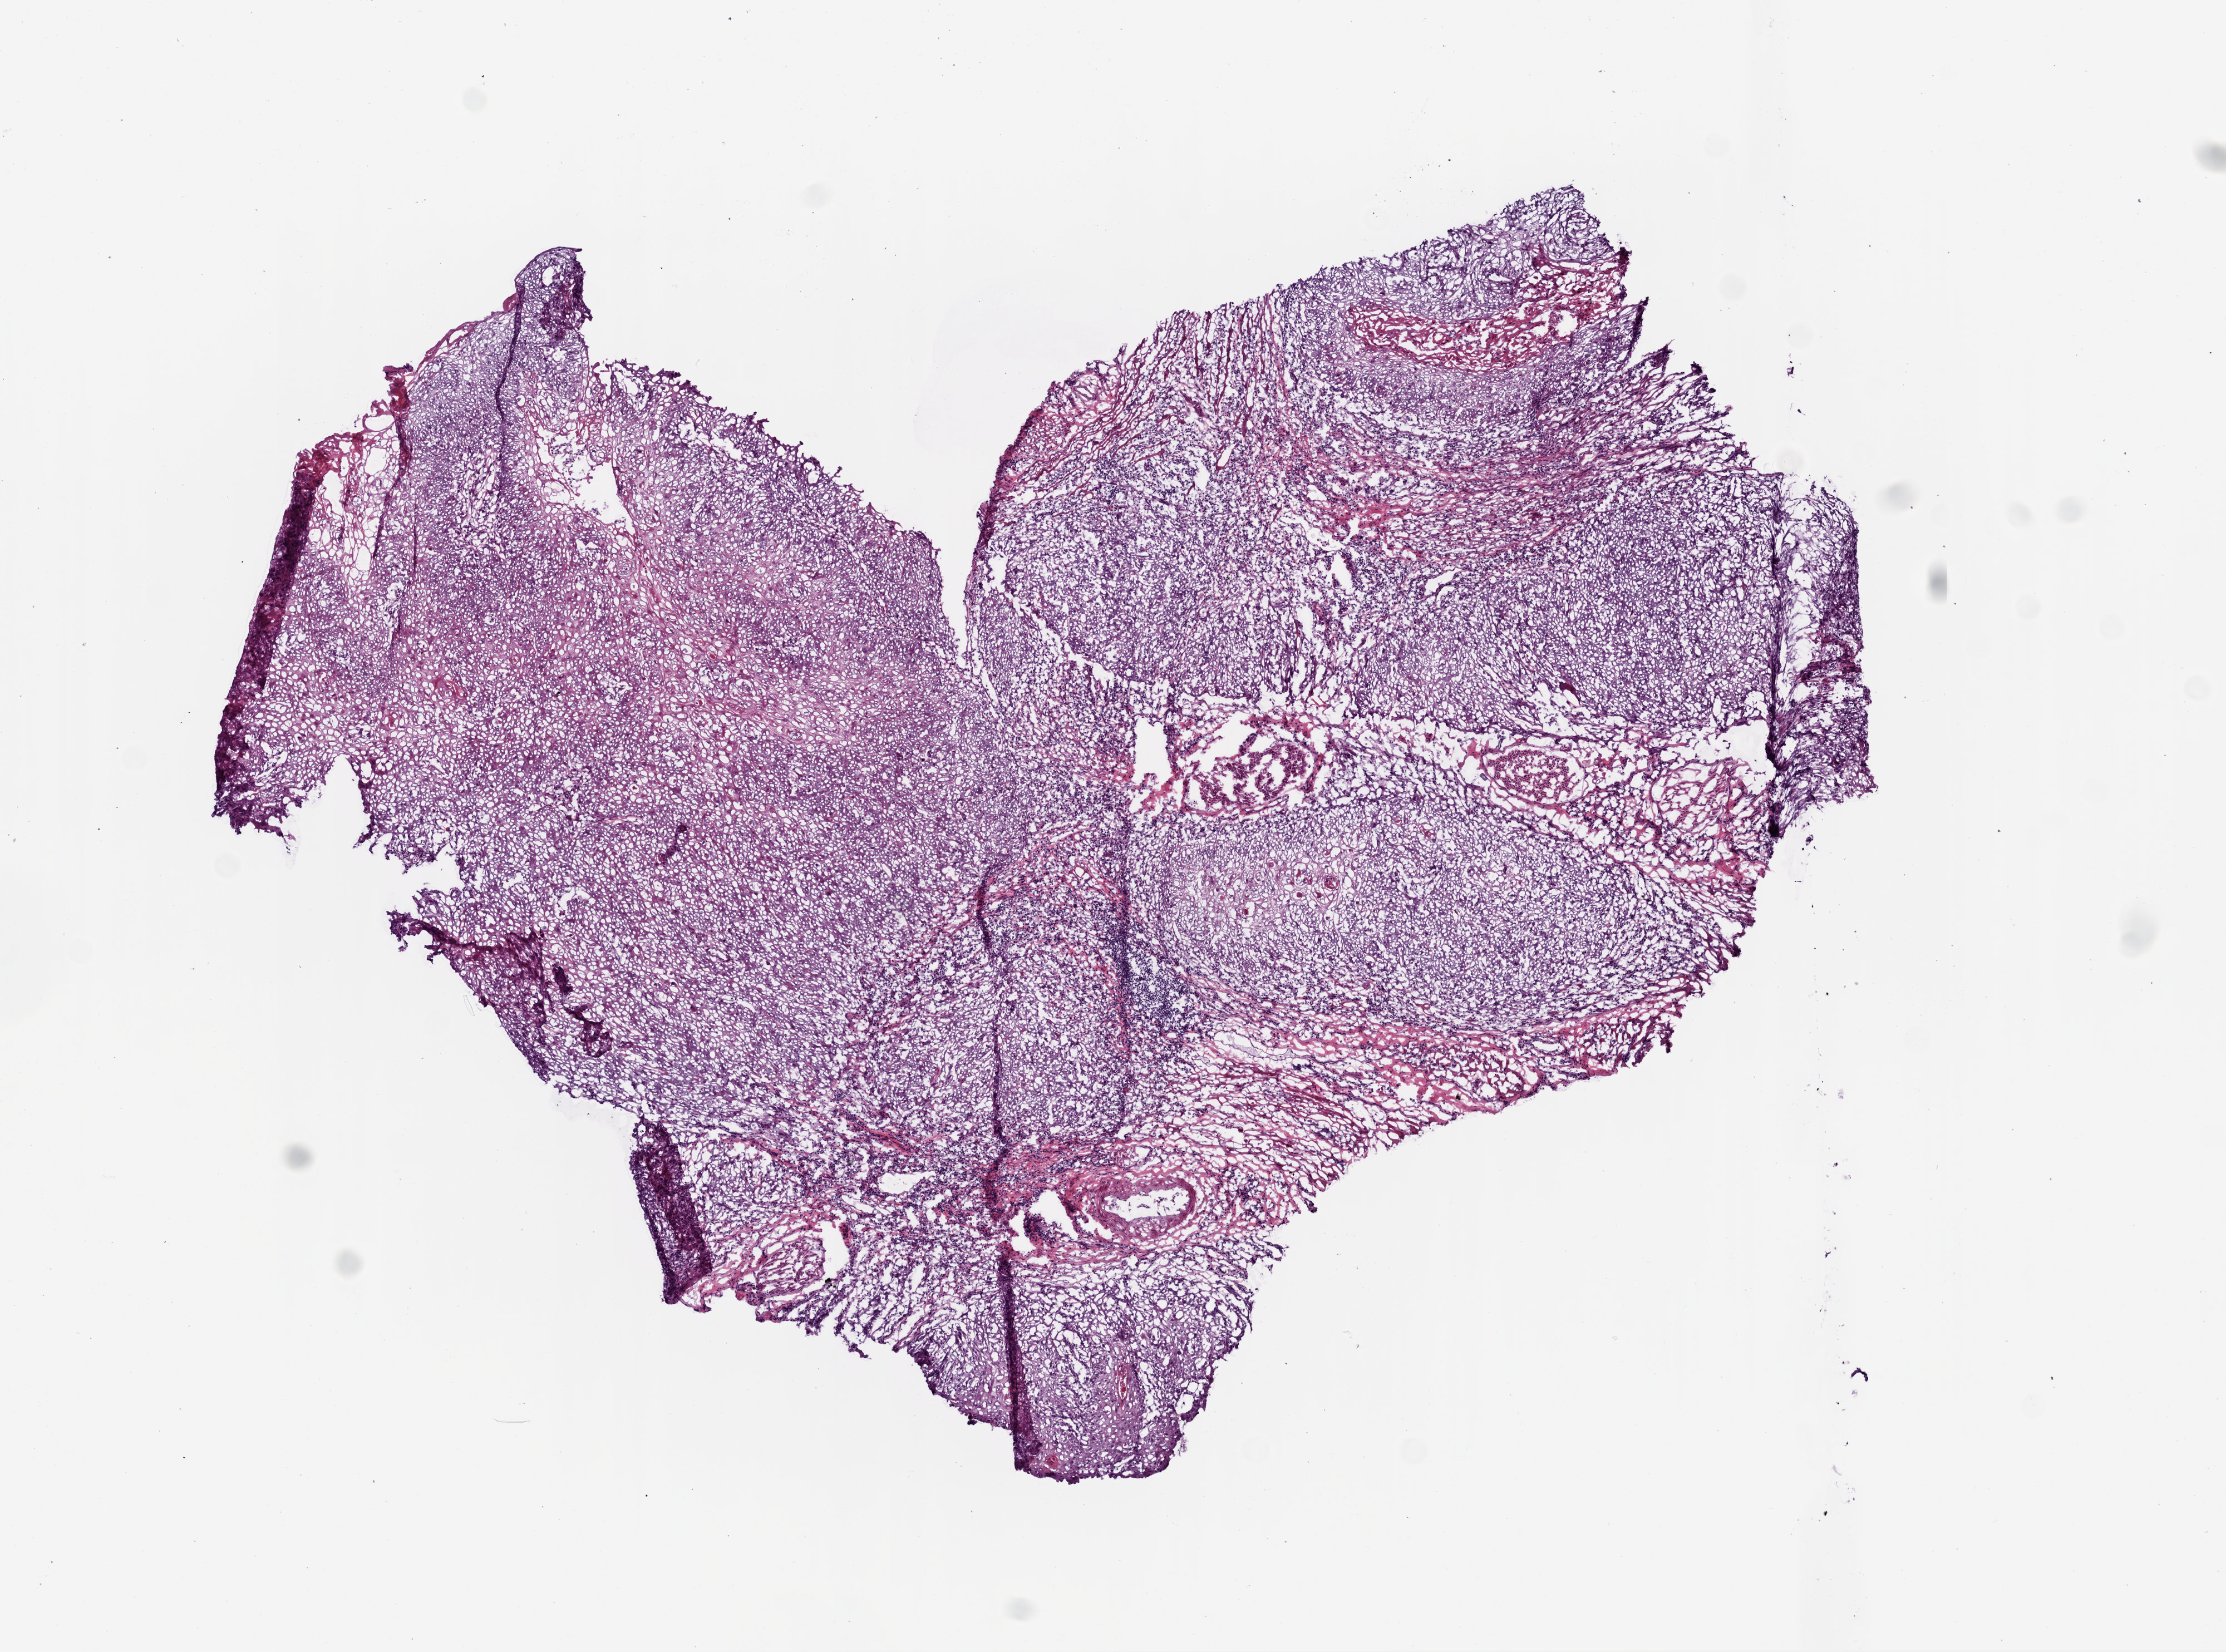
Whole-slide histology image, H&E-stained, shown as a low-resolution overview of the whole scanned area (about 8.0 x 6.0 mm), frozen section, head and neck, primary tumour sample. Female patient; age at initial diagnosis 61 years. Histologic grade: G2 (moderately differentiated). Composition of this section per pathologist review: tumour cells 95%, tumour nuclei 80%, normal cells 0%, stromal cells 0%, necrosis 5%. Inflammatory infiltration, as recorded: lymphocyte infiltration 10%, neutrophil infiltration 2%.
* AJCC pathologic stage: IVA (6th edition)
* pathologic diagnosis: Squamous cell carcinoma, NOS (tongue, NOS)
* lymph nodes positive (case pathology): 9 of 55 examined
* TNM: T3 N2c